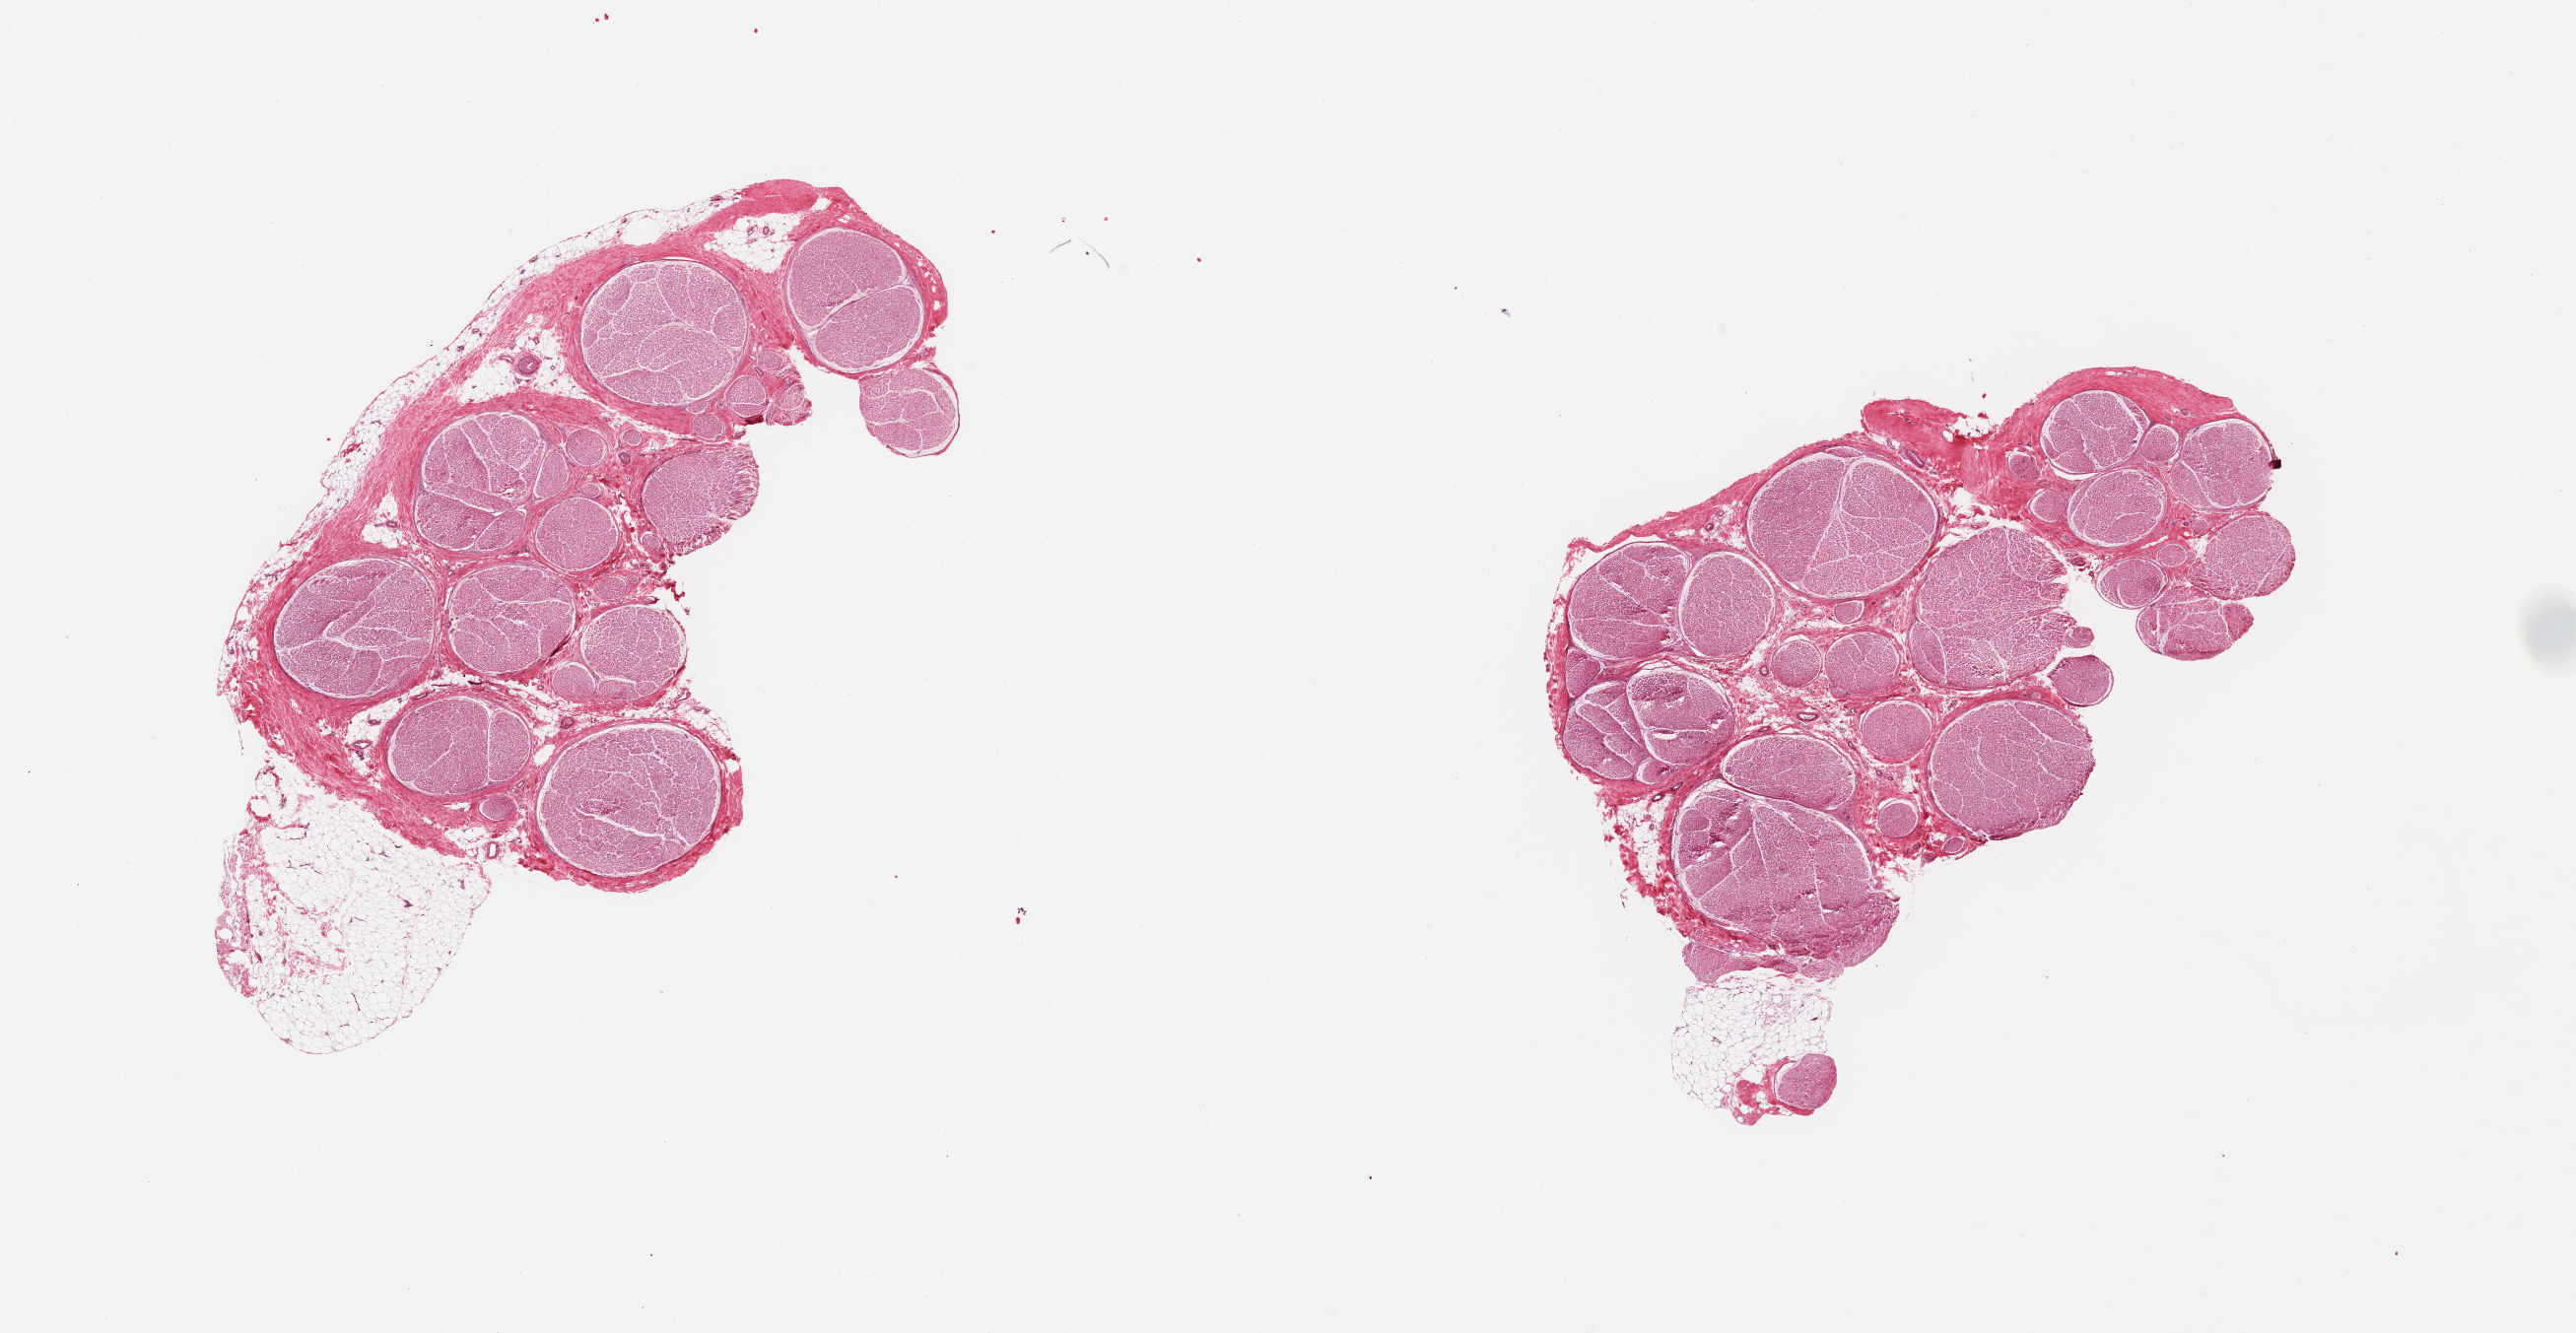
Digitized haematoxylin and eosin-stained section, brightfield — shown as a low-resolution overview of the whole scanned area (about 20.7 x 10.7 mm, acquisition: 20x scan). PAXgene-fixed, paraffin-embedded tissue. Section of tibial nerve (target tissue). Tissue donor sample. Donor sex: male.
- review note (as recorded): 2 pieces; 10% external and internal fat